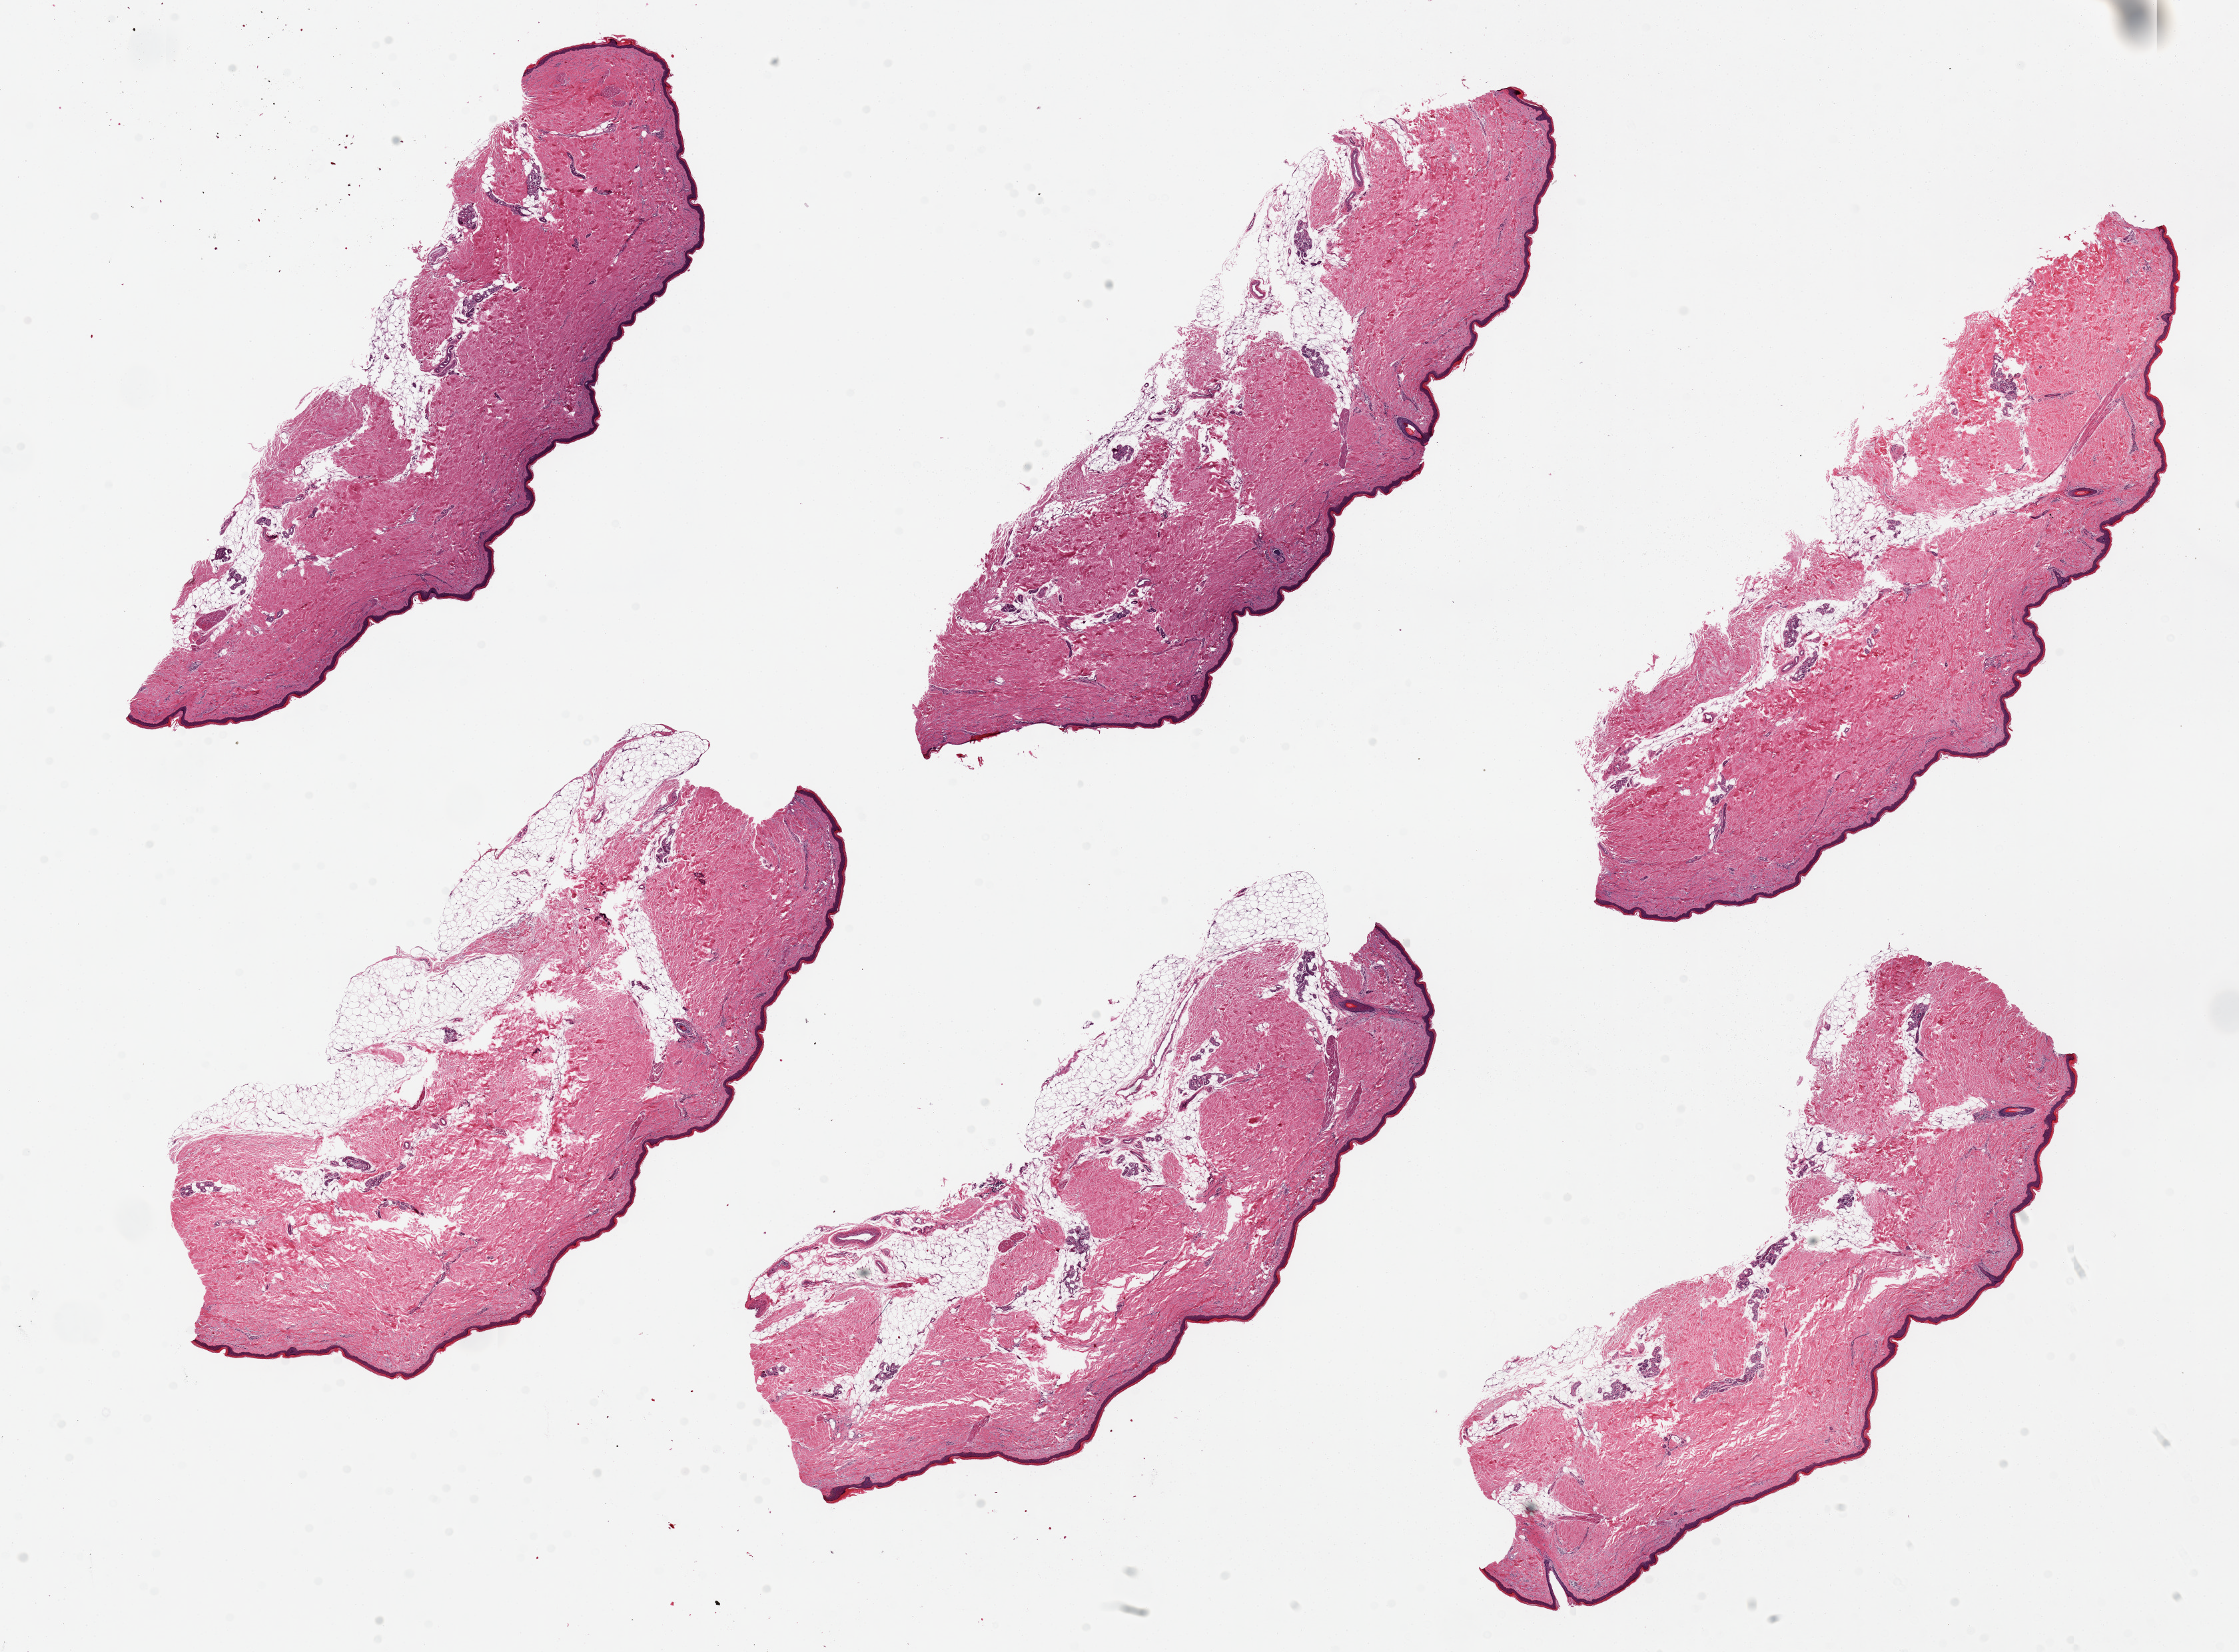
Whole-slide image, H&E stain, brightfield, low-resolution overview of the scanned area, about 26.6 x 19.6 mm. PAXgene-fixed, paraffin-embedded tissue. Sampled site (target tissue): skin of lower leg. Donor tissue sample. Female donor.
Pathologist's review note for this sample: 1 piece. 10x4mm; well trimmed subcutaneous fat; about 10% internal adipose.